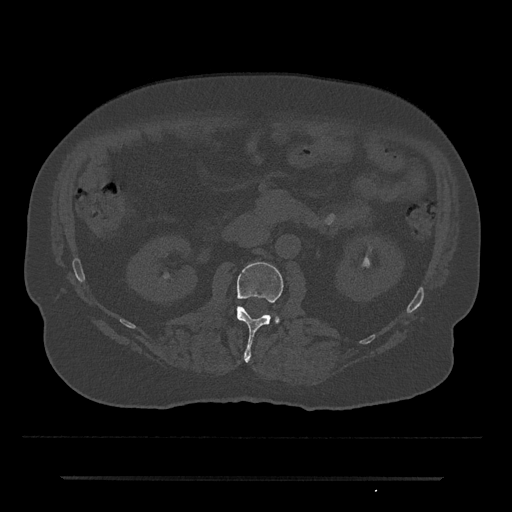
CT including the spine, one axial slice. Position 4 of 797 along the scan axis. Reconstruction kernel Br40s/3. Bone window (W 1800 / L 400 HU). 512 × 512 image matrix, field of view 437 × 437 mm. Male patient, age 69 years. From the clinical record (not read from this slice): primary cancer: prostate.
Outlined on this slice (semi-automatic segmentation, software-assisted and operator-edited):
- L2 vertebra: bounding box (x1, y1, x2, y2) in pixels: (237, 262, 283, 362)